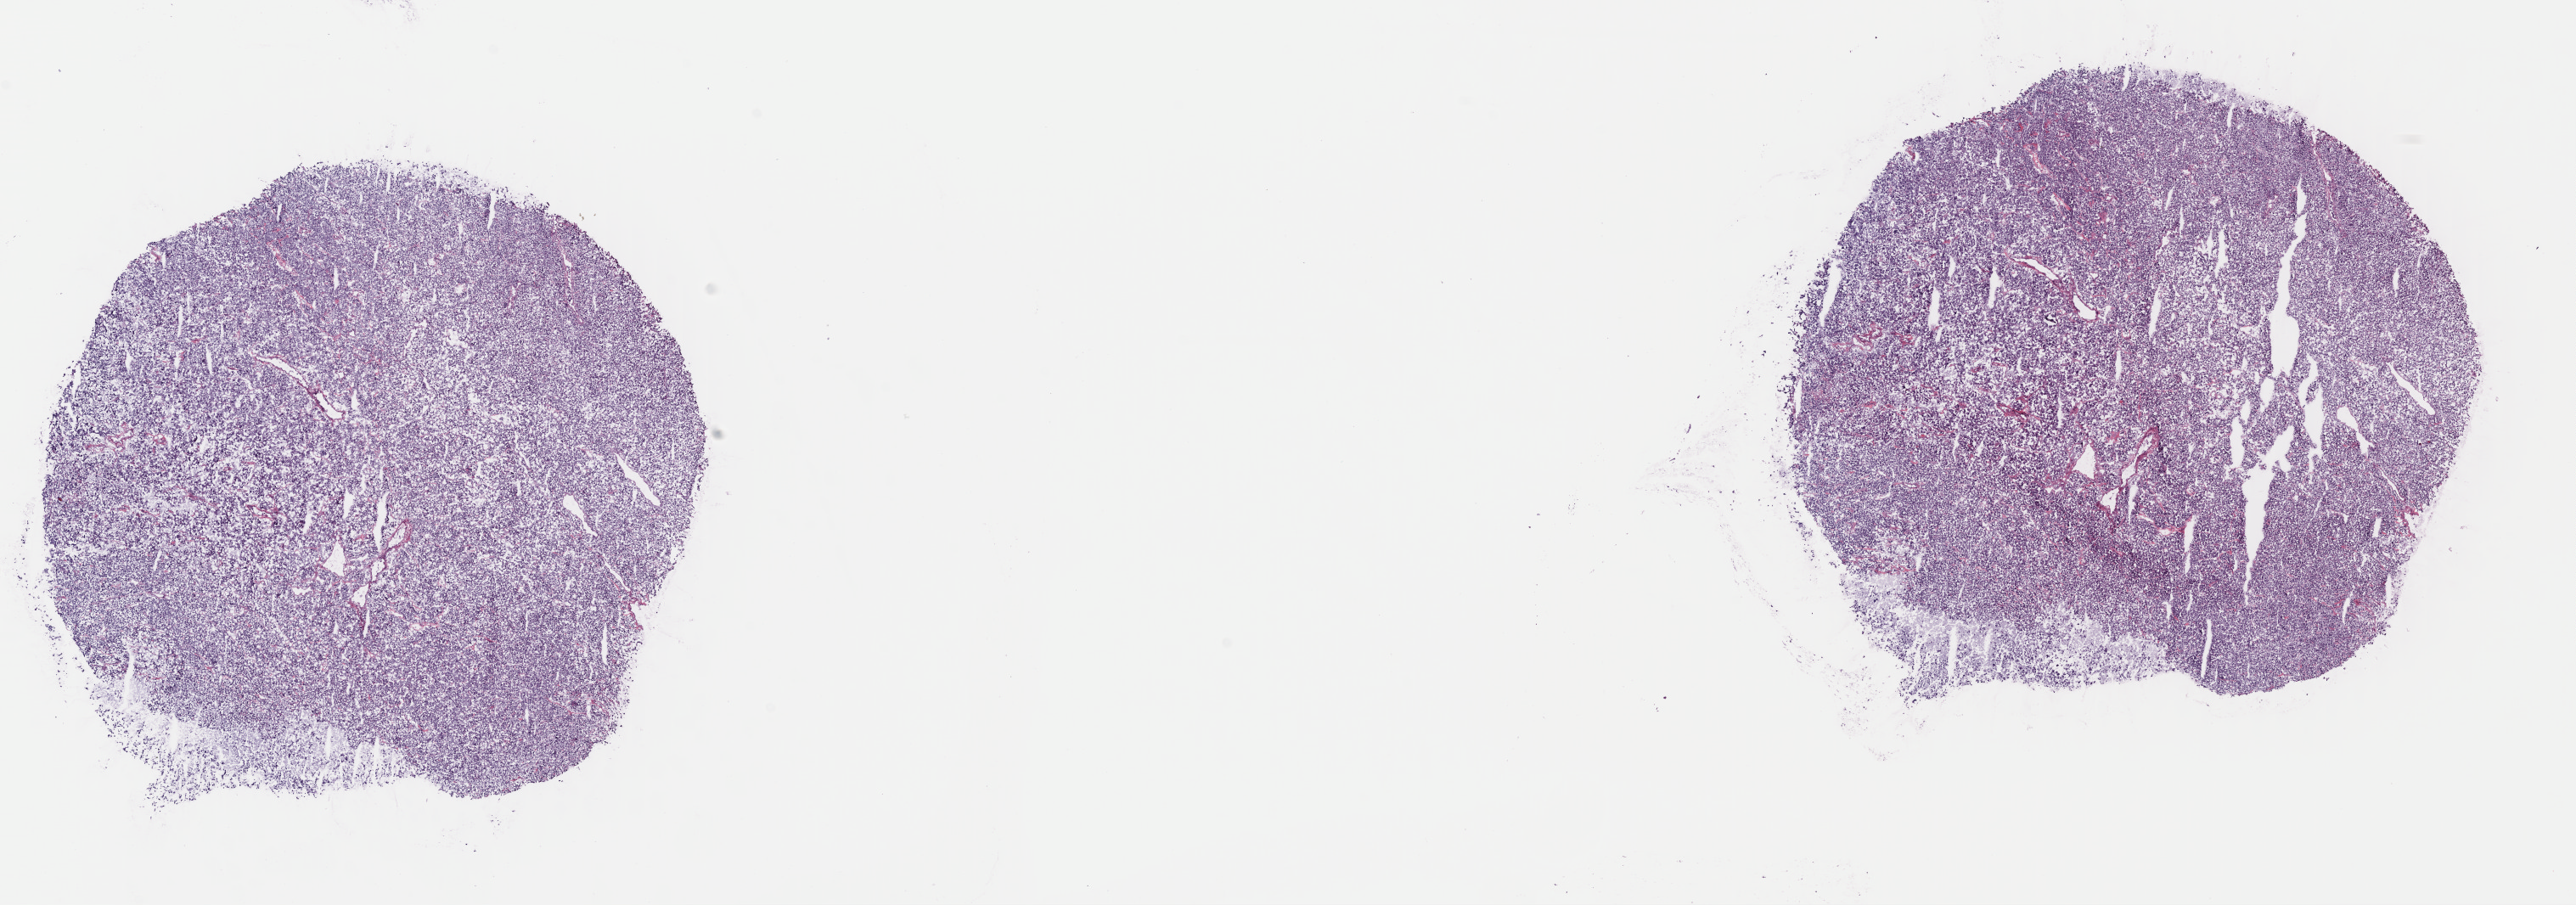
Hematoxylin and eosin (H&E) stained whole-slide image — whole scanned area (about 23.8 x 8.4 mm, acquisition: 40x scan) shown as a low-resolution overview, frozen section from the top of the tissue portion, sample: primary tumour, adrenal gland. Male patient; age at initial diagnosis 47 years. Pathologist review of this section (percent, as recorded): tumour cells 84%, tumour nuclei 90%, normal cells 0%, stromal cells 12%, necrosis 4%. Inflammatory infiltration, as recorded: lymphocyte infiltration 2%, monocyte infiltration 0%, neutrophil infiltration 0%.
Histologic diagnosis: Pheochromocytoma, NOS.